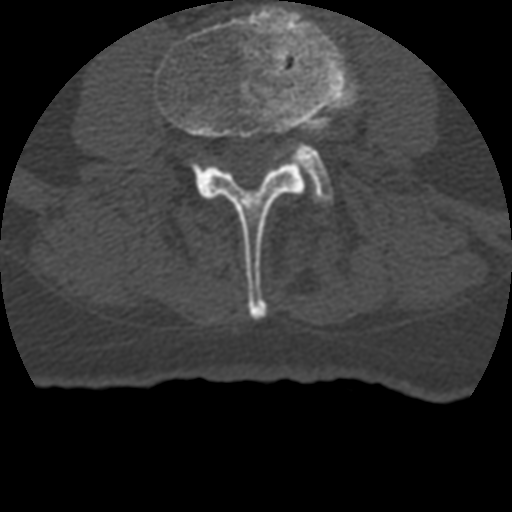
CT including the spine, one axial slice; position 84 of 399 along the scan axis; reconstruction kernel STANDARD; 120 kVp; bone window (W 1800 / L 400 HU); 1.25 mm slice thickness; 512 × 512 image matrix, field of view 160 × 160 mm. Patient age 69 years. From the clinical record (not read from this slice): primary cancer: prostate.
Structures marked on this image (semi-automatically segmented with operator editing):
- L3 vertebra: bounding box <155,5,351,319> (left, top, right, bottom; pixels)
- L4 vertebra: <292,144,334,206>